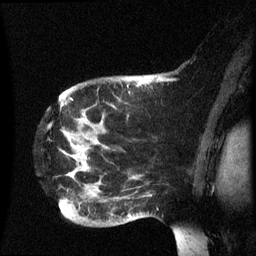
Breast MRI (dynamic contrast-enhanced), one sagittal slice; slice 49 of 60 in the series (ordered by position); dynamic contrast-enhanced series, image 2 of 3 at this slice position (ordered by acquisition); 1.5 T; TE 4.2 ms, TR 8.4 ms; 2.5 mm slice thickness; 256 × 256 image matrix, field of view 220 × 220 mm. Female patient, age 49 years.
Outlined on this slice (semi-automatic segmentation, software-assisted and operator-edited):
- analysis volume of interest (the breast-tissue region the enhancement analysis was run in; not a lesion): box from (x=50, y=74) to (x=185, y=235) px
- tumour enhancement mask (voxels above the 70 % enhancement threshold inside the analysis volume of interest): (x=131, y=82)–(x=143, y=217)